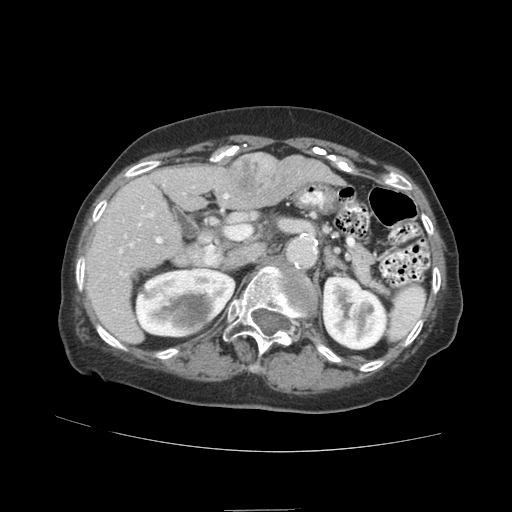
Contrast-enhanced abdominal CT (liver protocol), one axial slice. Slice 49 of 89 in the series (ordered by position). 140 kVp. Soft-tissue window (W 400 / L 40 HU). 2.5 mm slice thickness. 512 × 512 image matrix. Case-level facts recorded for this patient, not image findings: diagnosis: hepatocellular carcinoma (patient treated with transarterial chemoembolisation; whether this scan precedes or follows treatment is not stated here); TNM stage (as recorded): Stage-II; Child-Pugh class: A; tumour differentiation: moderately differentiated; tumour nodularity: multinodular.
Structures marked on this image (semi-automatic segmentation, software-assisted and operator-edited):
- liver parenchyma outside the tumour (the mass and vessels are separate outlines, so this box may not span the whole liver): bounding box [x1, y1, x2, y2] px = [86, 160, 340, 342]
- mass: [229, 153, 286, 207]
- liver vessels: [103, 185, 164, 312]